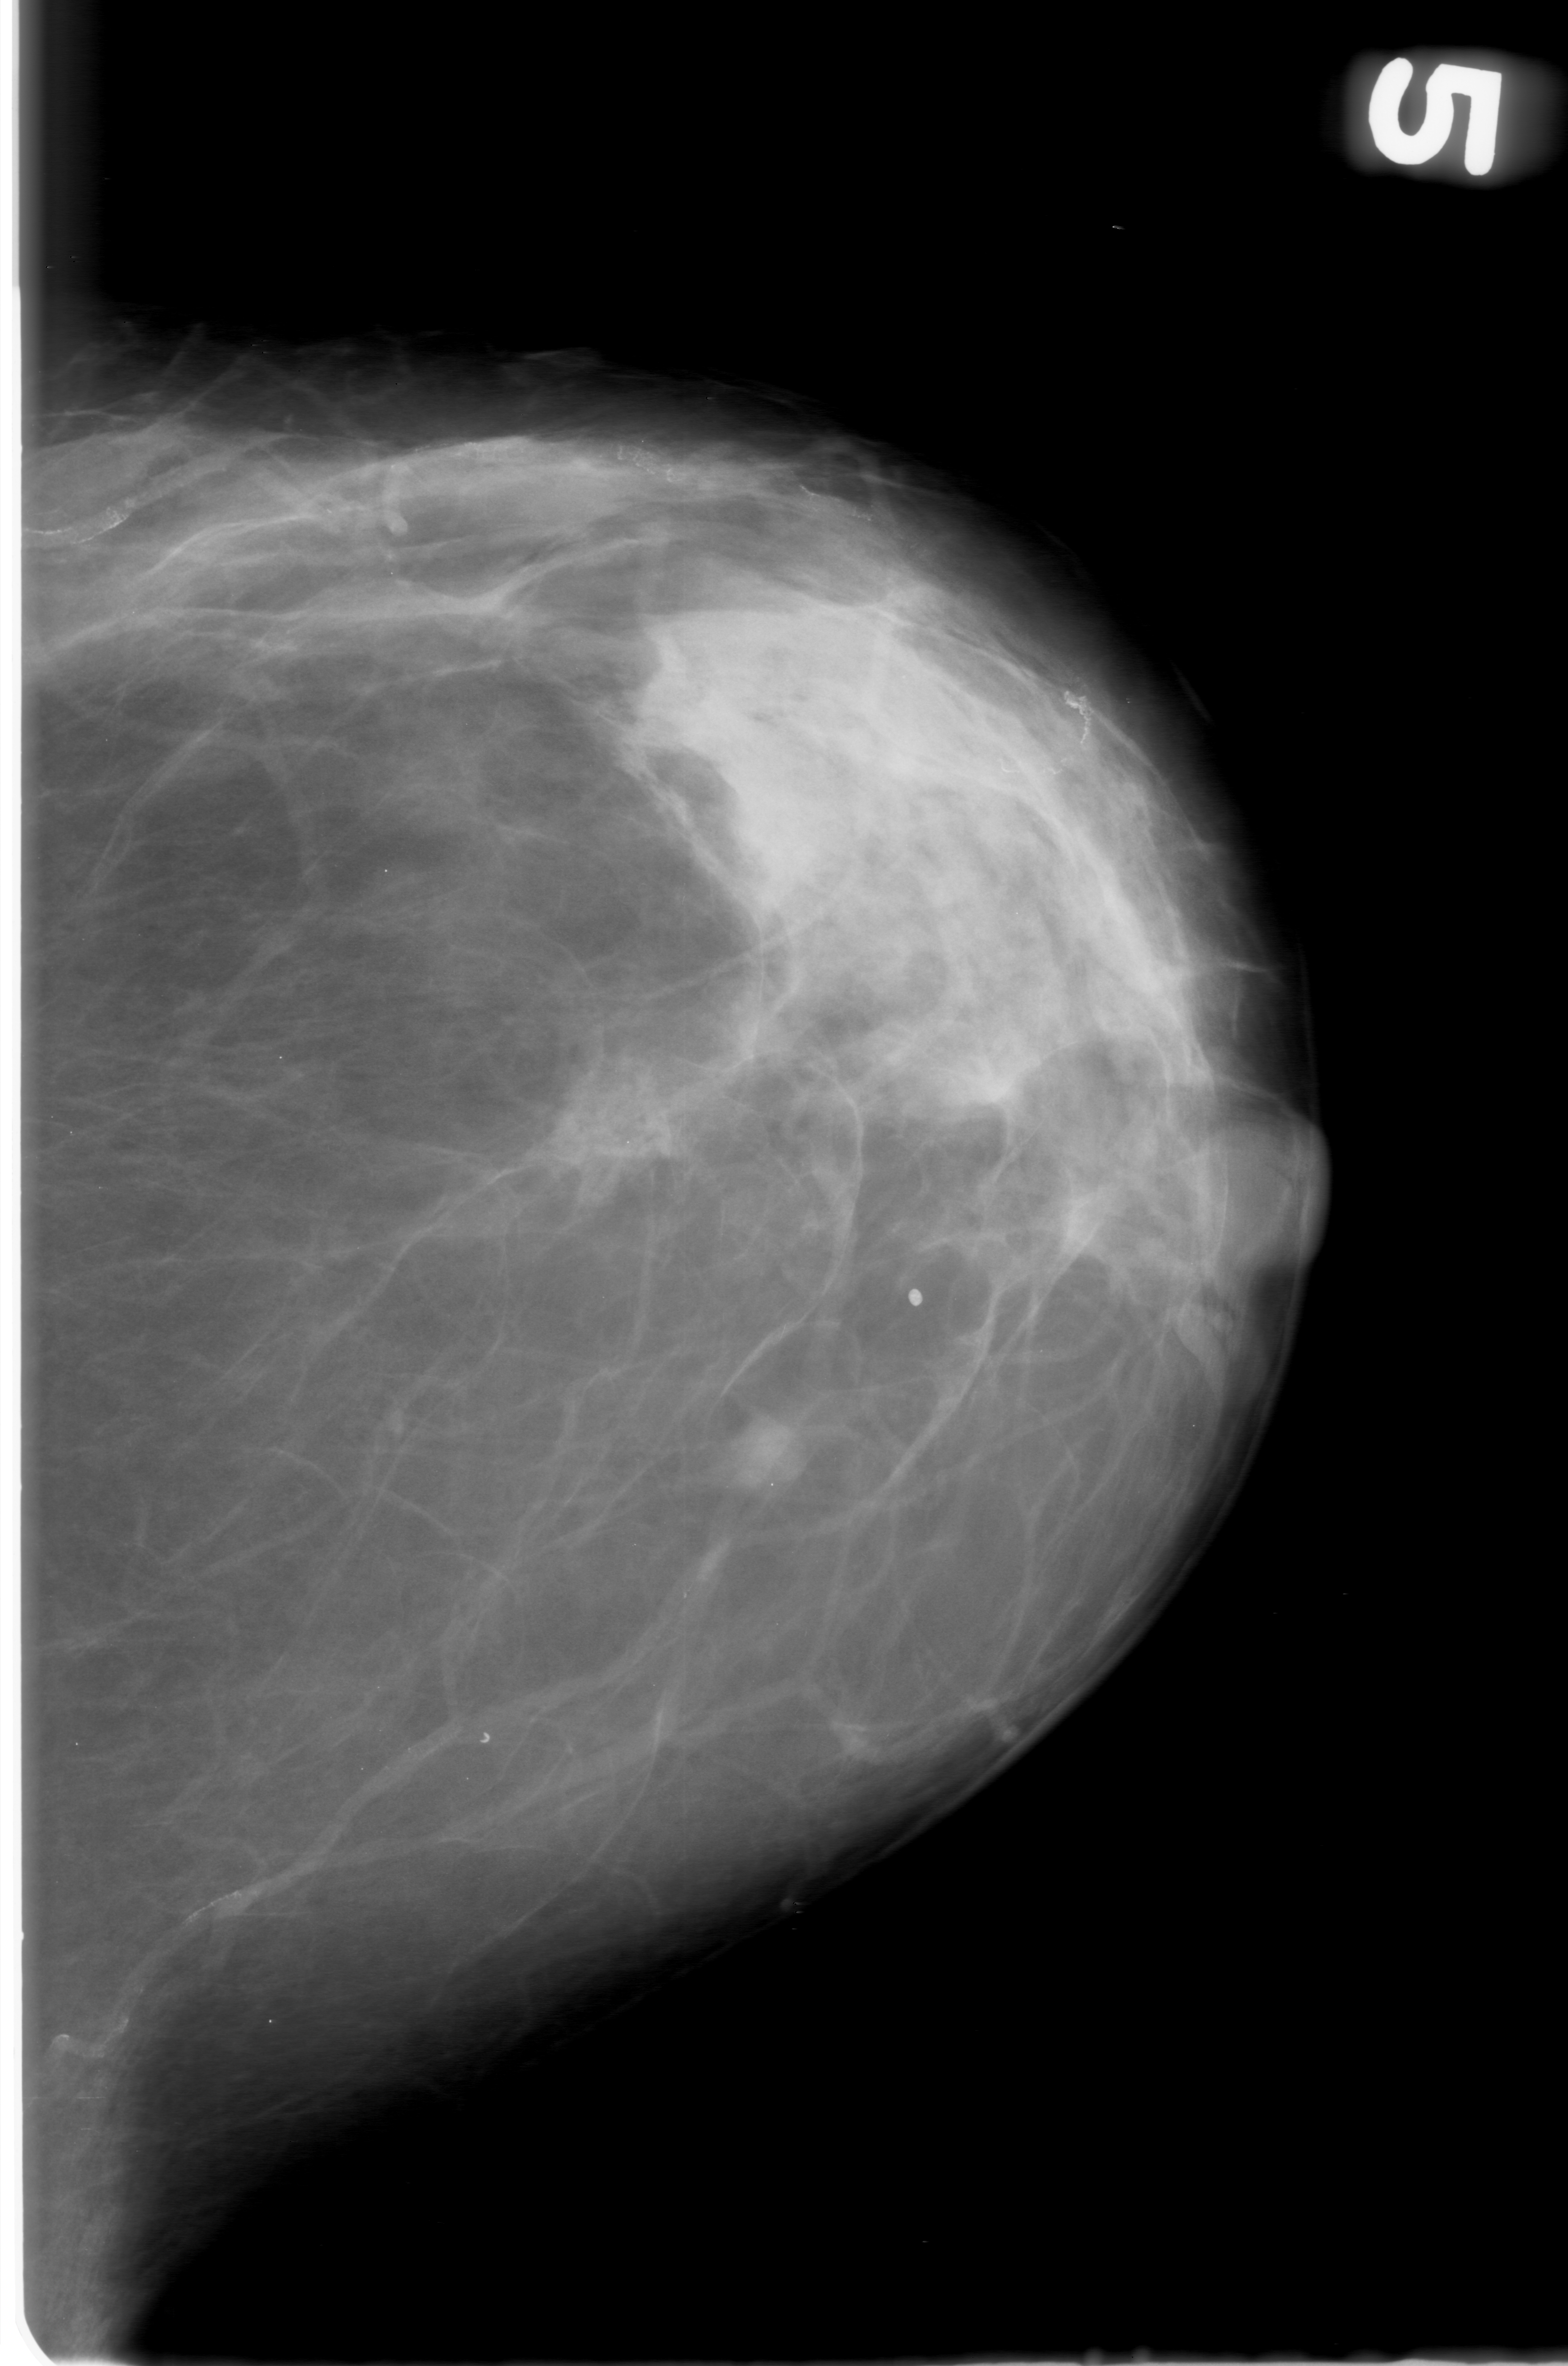
Scanned film-screen mammogram; left breast; CC view; breast composition: scattered fibroglandular densities (BI-RADS density category 2 of 4); 1568 × 2366 image matrix.
Expert-marked regions of interest on this film, with their recorded descriptors:
- mass, shape round, margins obscured; BI-RADS assessment category 0 (incomplete: needs additional imaging); pathology (as recorded): benign: bounding box [x1, y1, x2, y2] px = [714, 1400, 819, 1503]